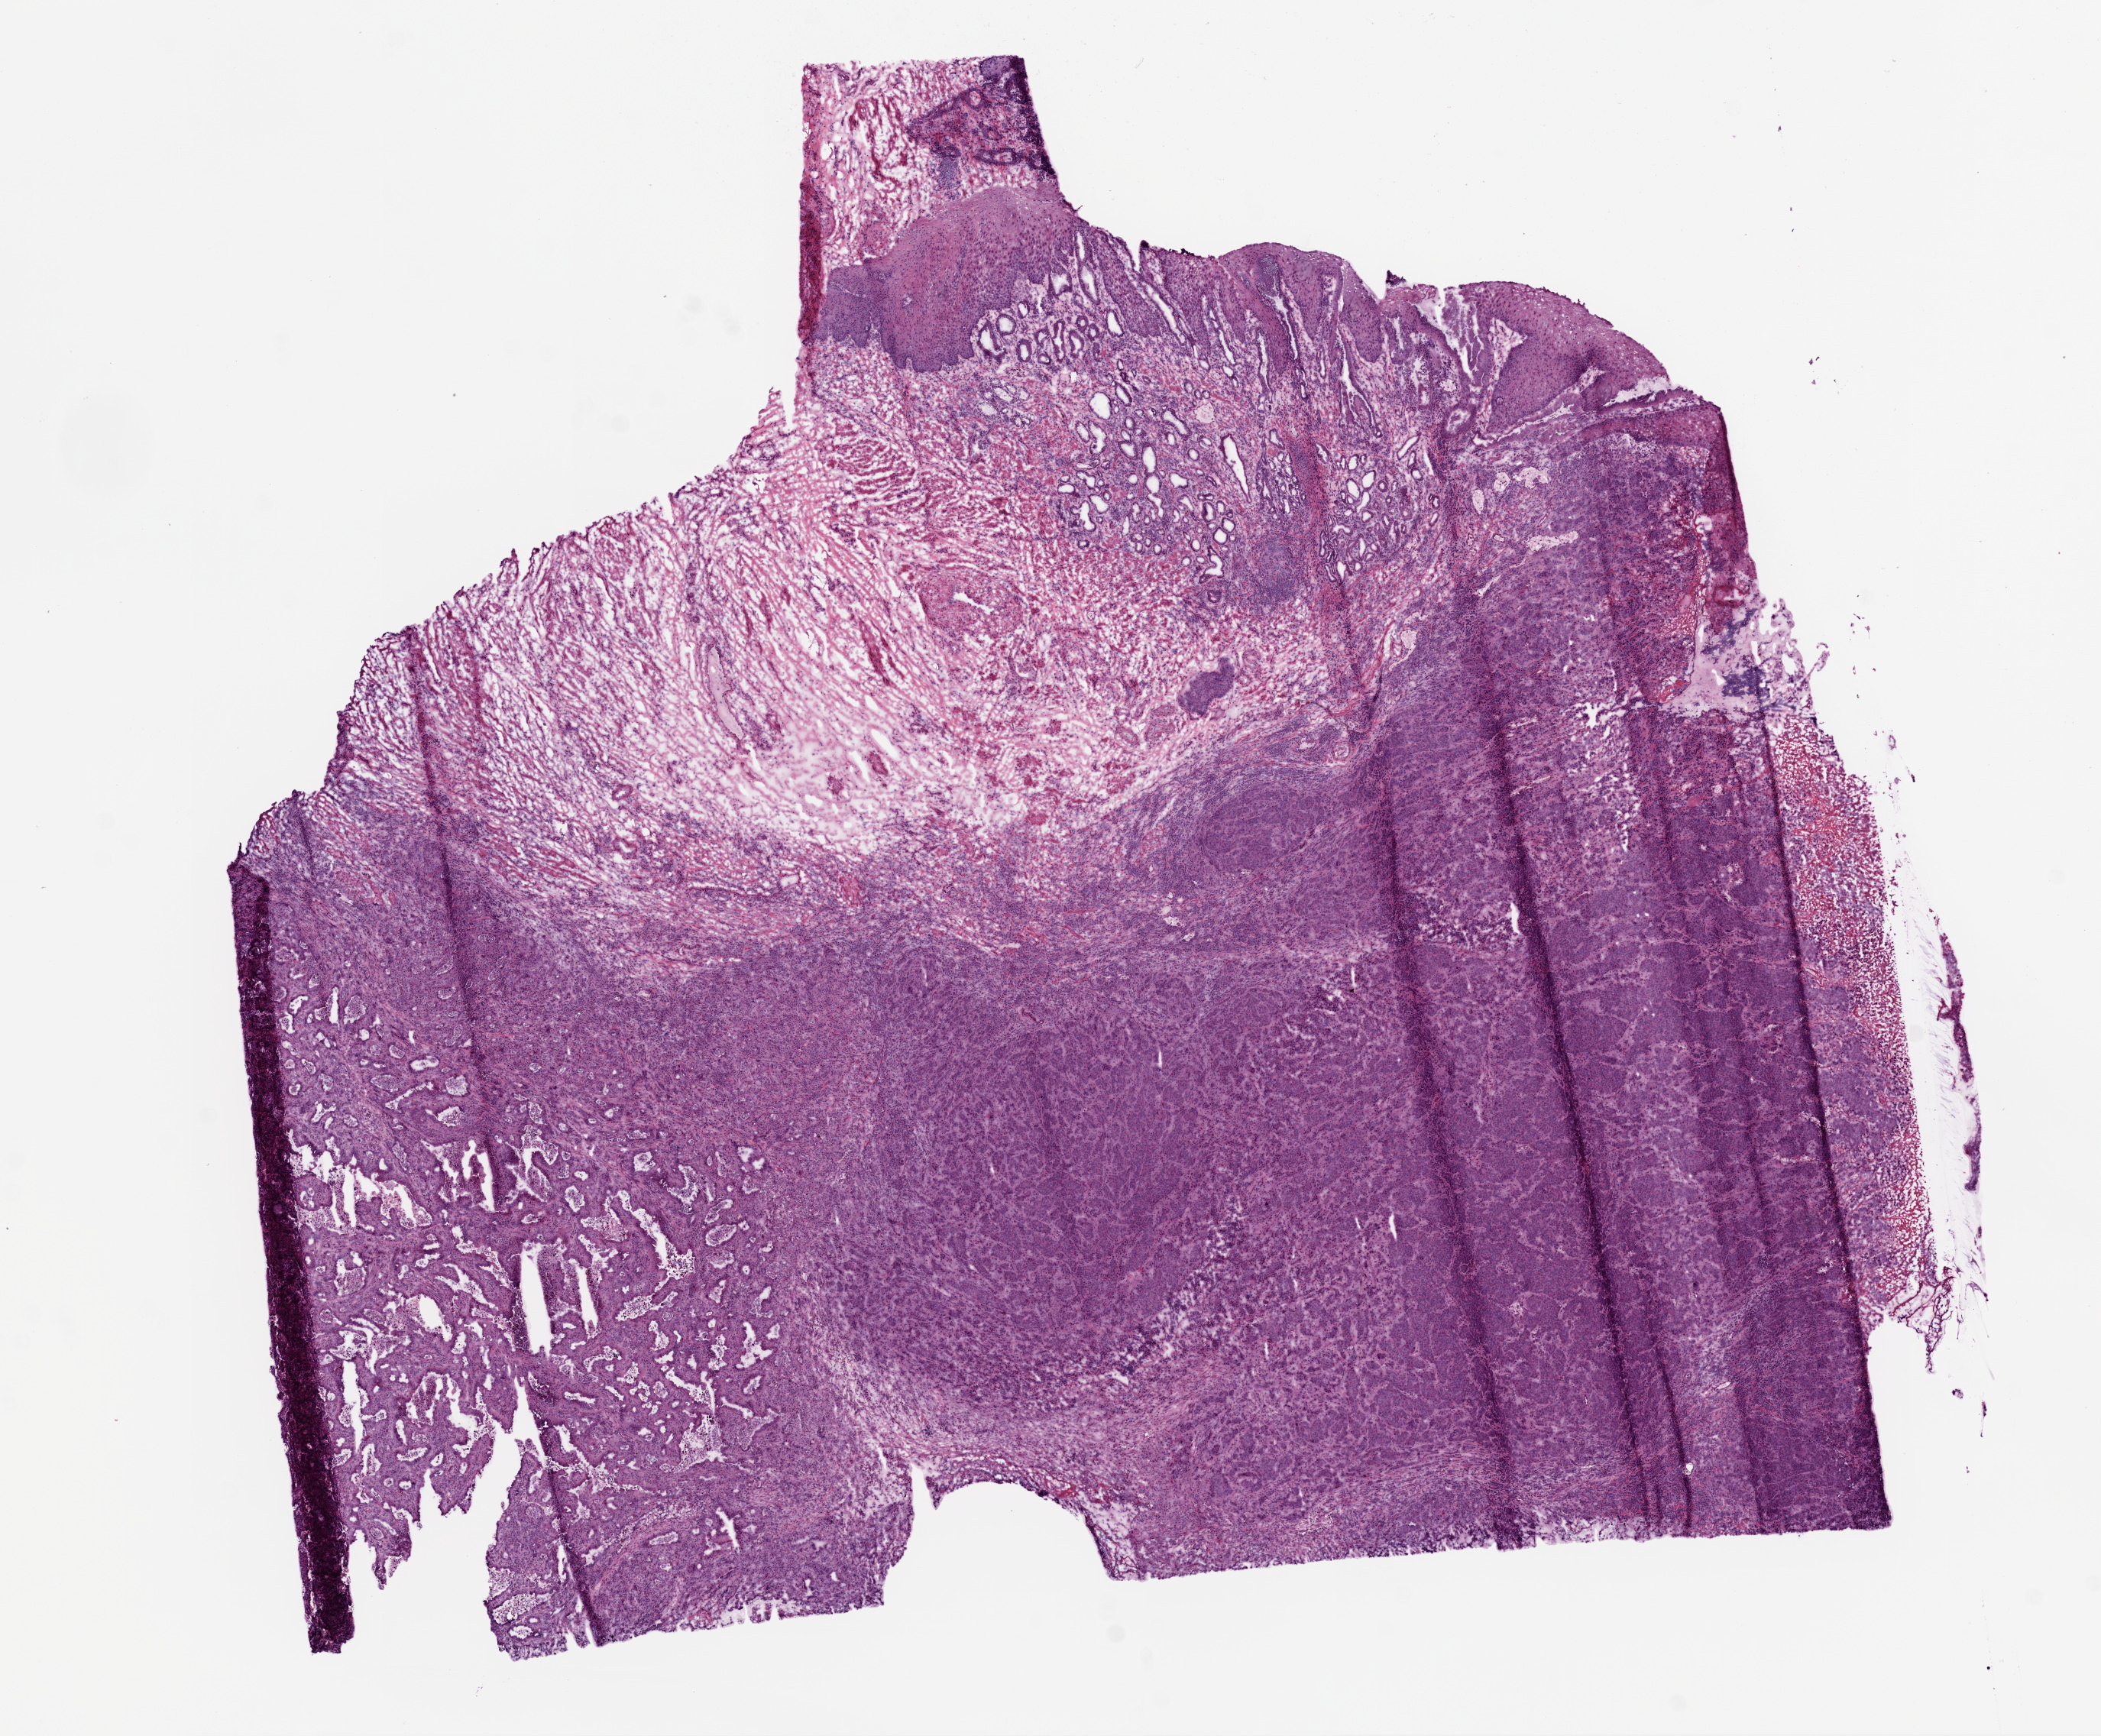
Digitized H&E-stained tissue section (whole slide), whole scanned area (about 11.0 x 9.1 mm) shown as a low-resolution overview, frozen section from the bottom of the tissue portion, primary tumour sample from the stomach. Female, age 58 years at initial diagnosis. Histologic grade: G3 (poorly differentiated). Composition of this section per pathologist review: tumour cells 77%, tumour nuclei 75%, normal cells 5%, stromal cells 15%, necrosis 3%.
Histologic diagnosis: Adenocarcinoma, intestinal type (cardia, NOS). AJCC pathologic stage: IB (6th edition). Lymph nodes positive (case pathology): 0 of 17 examined. TNM: T2a N0 M0.